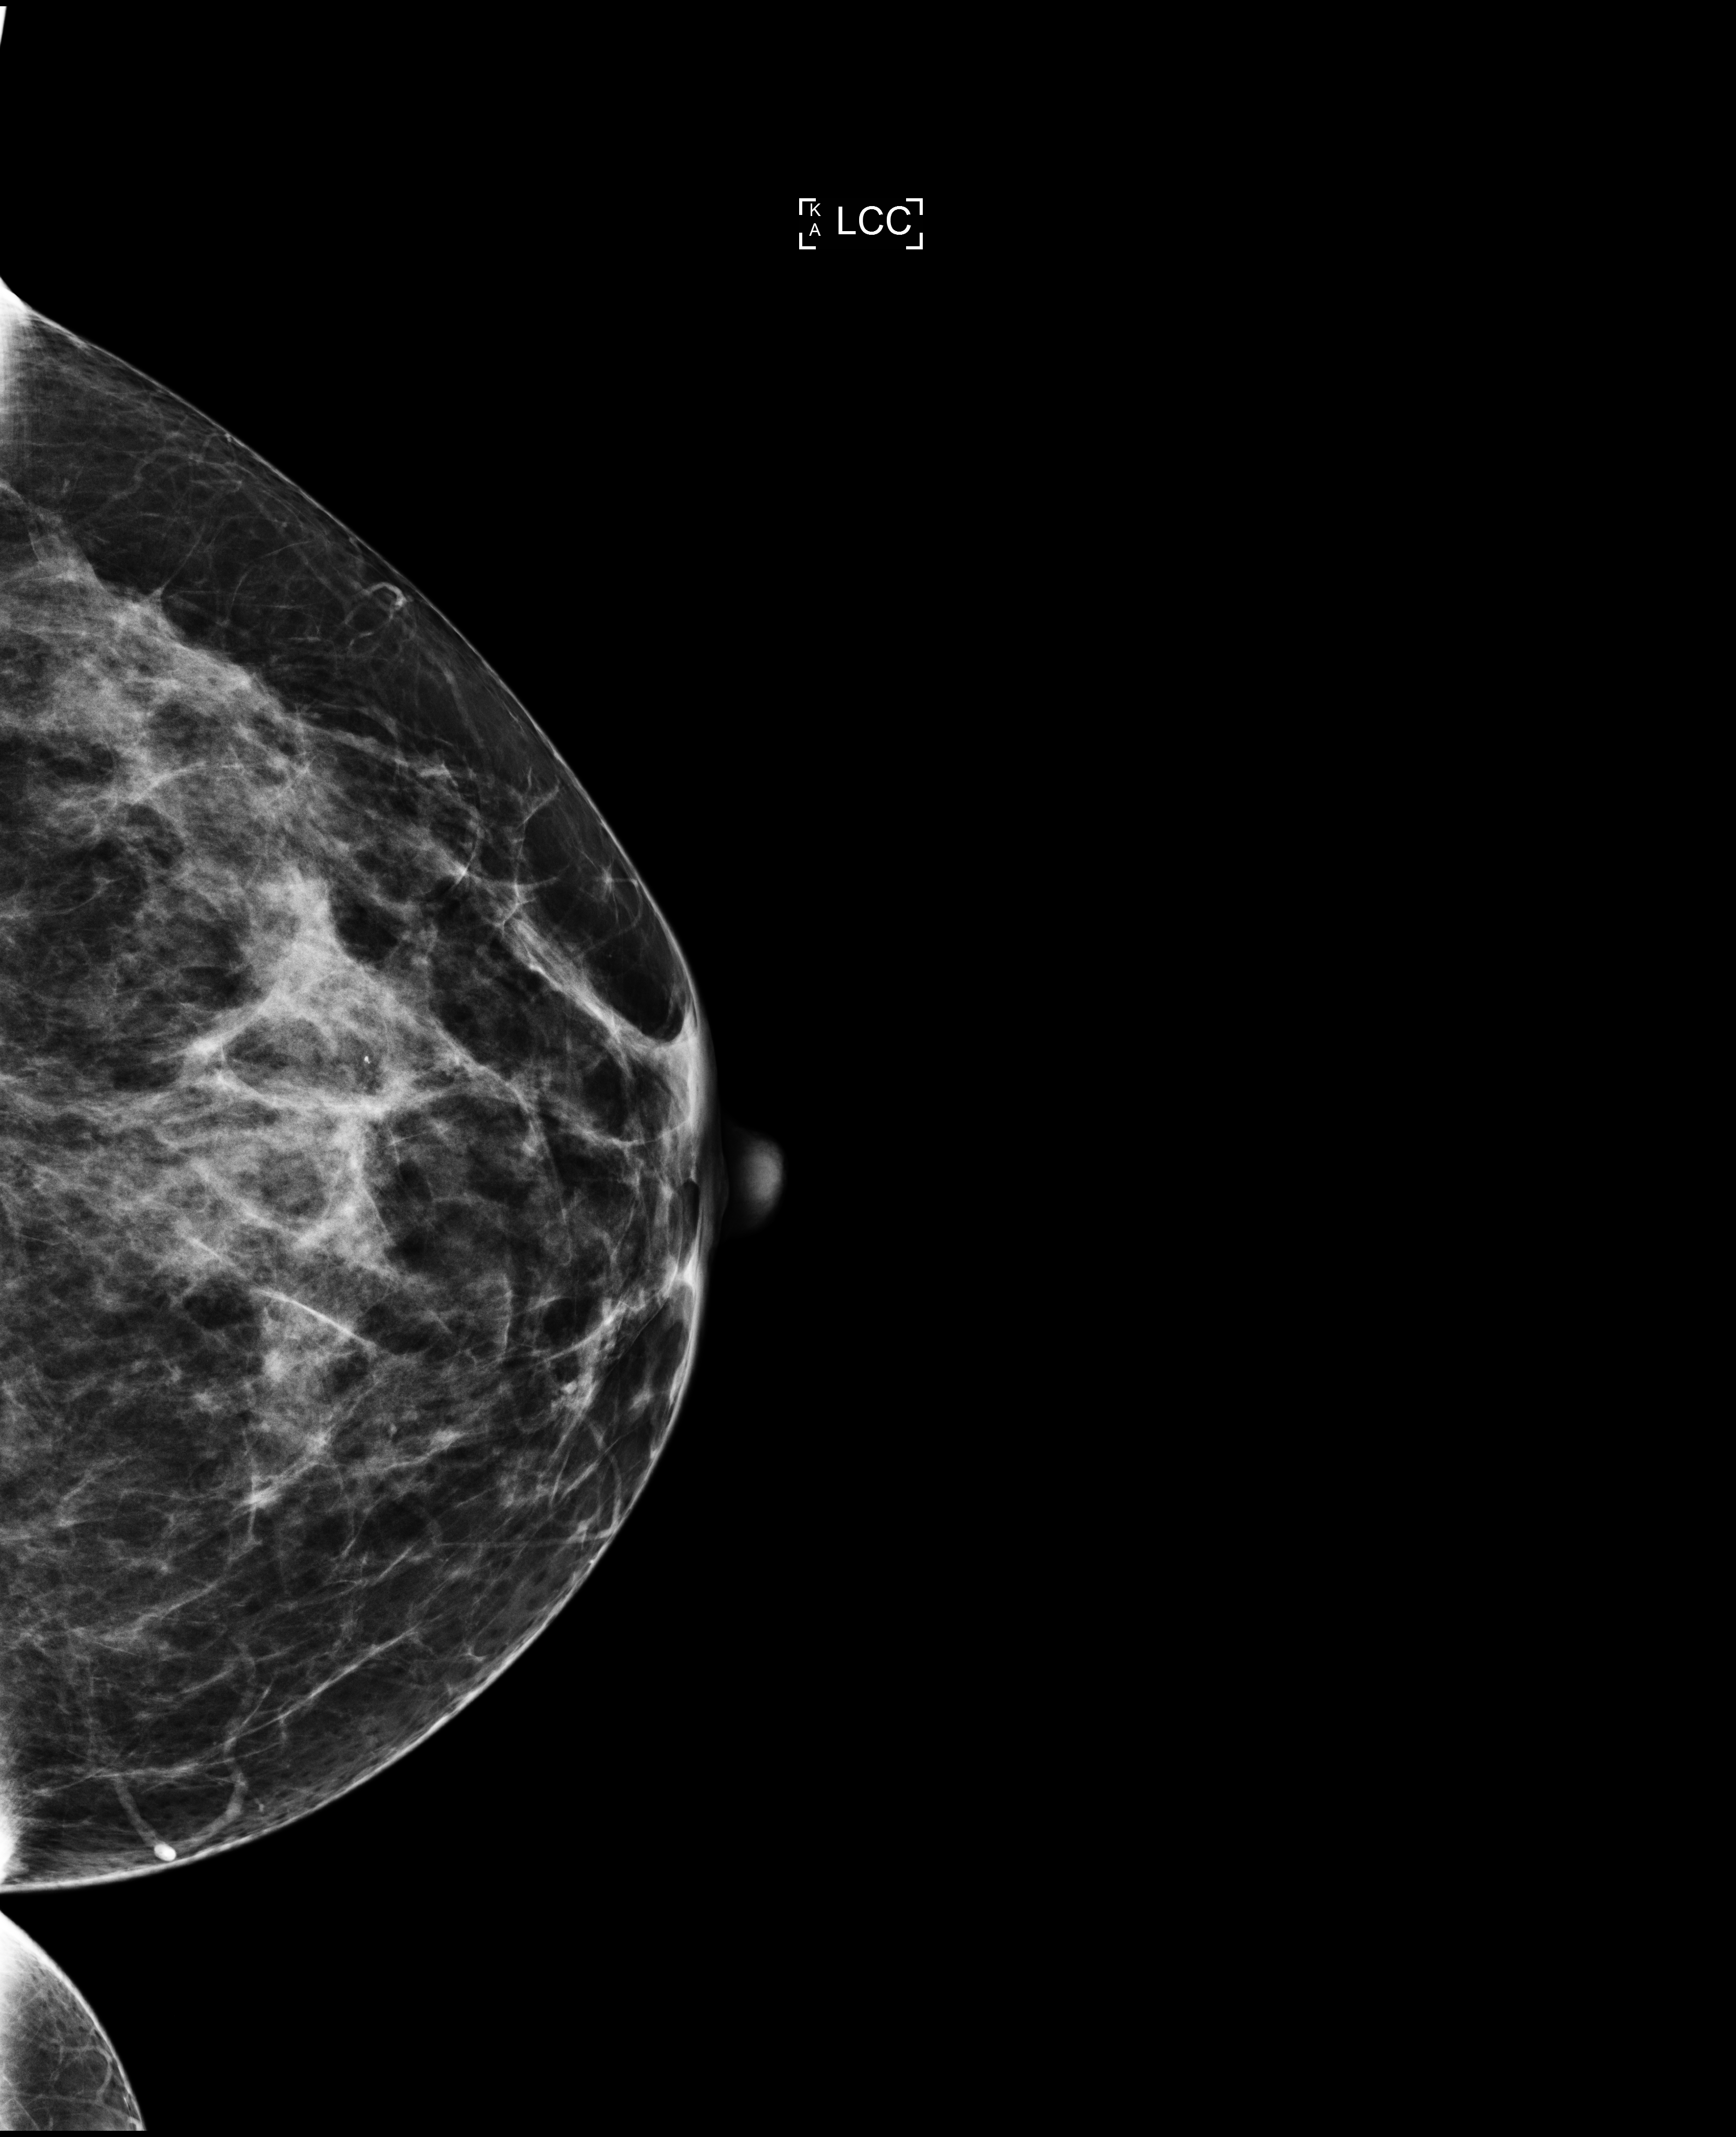
Screening examination; compressed breast thickness 63 mm. Female patient, age 47 years.
Image type: full-field digital mammogram. Breast: left. Projection: cranio-caudal projection.